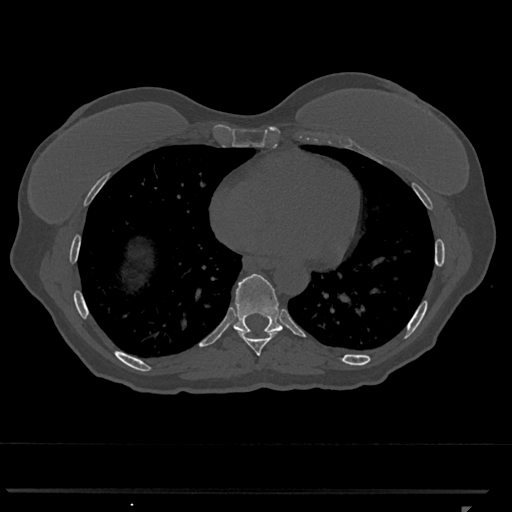
CT including the spine, one axial slice; slice 642 of 793 in the series (ordered by position); 120 kVp; bone window (W 1800 / L 400 HU); 512 × 512 image matrix, field of view 380 × 380 mm. Patient: female, 62 years. From the clinical record (not read from this slice): primary cancer: renal.
Annotated regions visible in this slice (semi-automatically segmented with operator editing):
- T8 vertebra: box from (x=238, y=332) to (x=278, y=356) px
- T9 vertebra: (x=232, y=274)–(x=283, y=334)